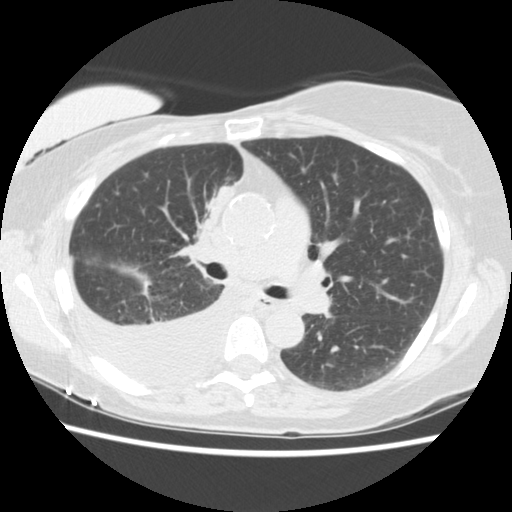
Low-dose screening chest CT, one axial slice; slice 90 of 157 in the series (ordered by position); 120 kVp; lung window (W 1500 / L -600 HU); 2.5 mm slice thickness; 512 × 512 image matrix, field of view 330 × 330 mm.
Annotated regions visible in this slice (expert manual segmentation):
- lesion 1 (tumor, upper lobe of right lung): bounding box (x1, y1, x2, y2) in pixels: (206, 185, 234, 223)